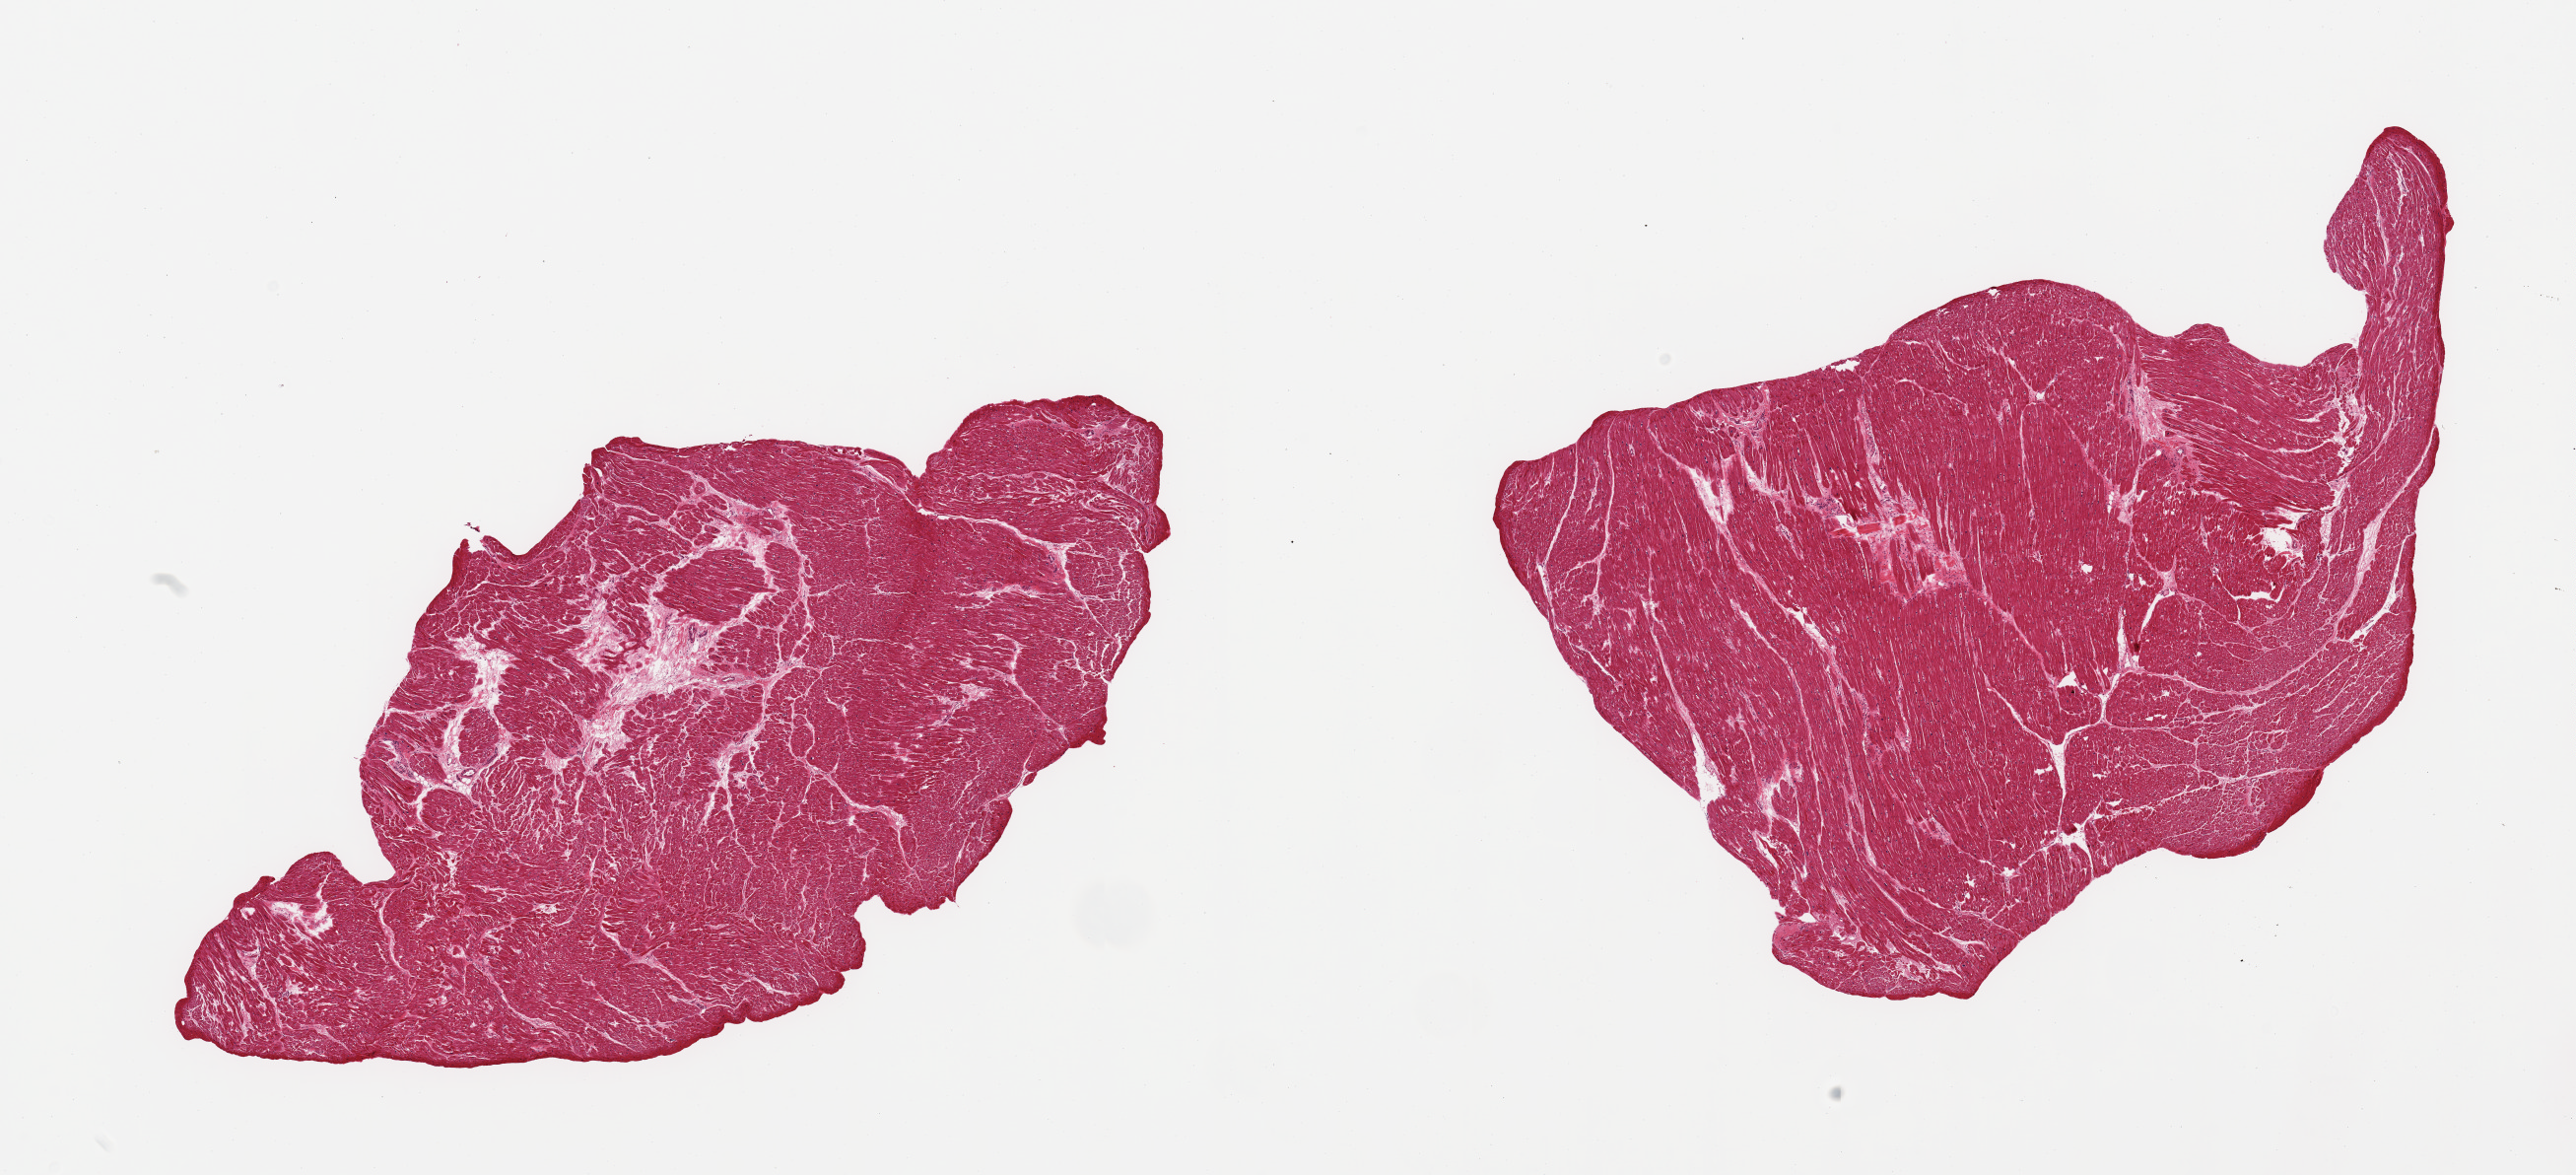
Digitized H&E-stained section, low-resolution overview of the scanned area, about 20.7 x 9.4 mm. PAXgene-fixed, paraffin-embedded tissue. Target tissue: heart. Tissue donor sample. Male donor.
* reviewer comment on this tissue sample: 2 pieces; contraction bands